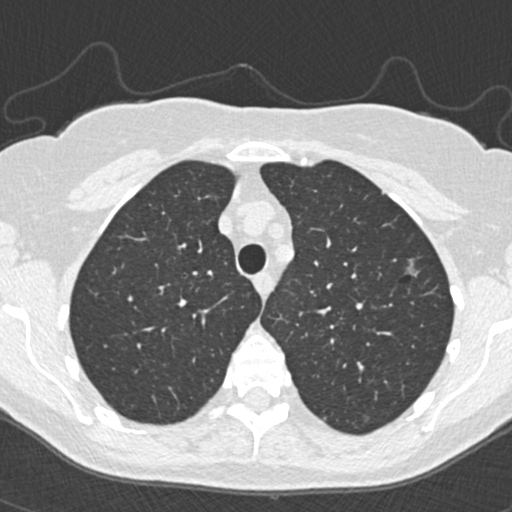
Low-dose screening chest CT, one axial slice. Slice 278 of 350 in the series (ordered by position). Lung window (W 1500 / L -600 HU). 1 mm slice thickness. 512 × 512 image matrix, field of view 298 × 298 mm.
Annotated regions visible in this slice (outlined manually by an expert reader):
- lesion 3 (tumor, upper lobe of left lung): box from (x=405, y=265) to (x=418, y=276) px